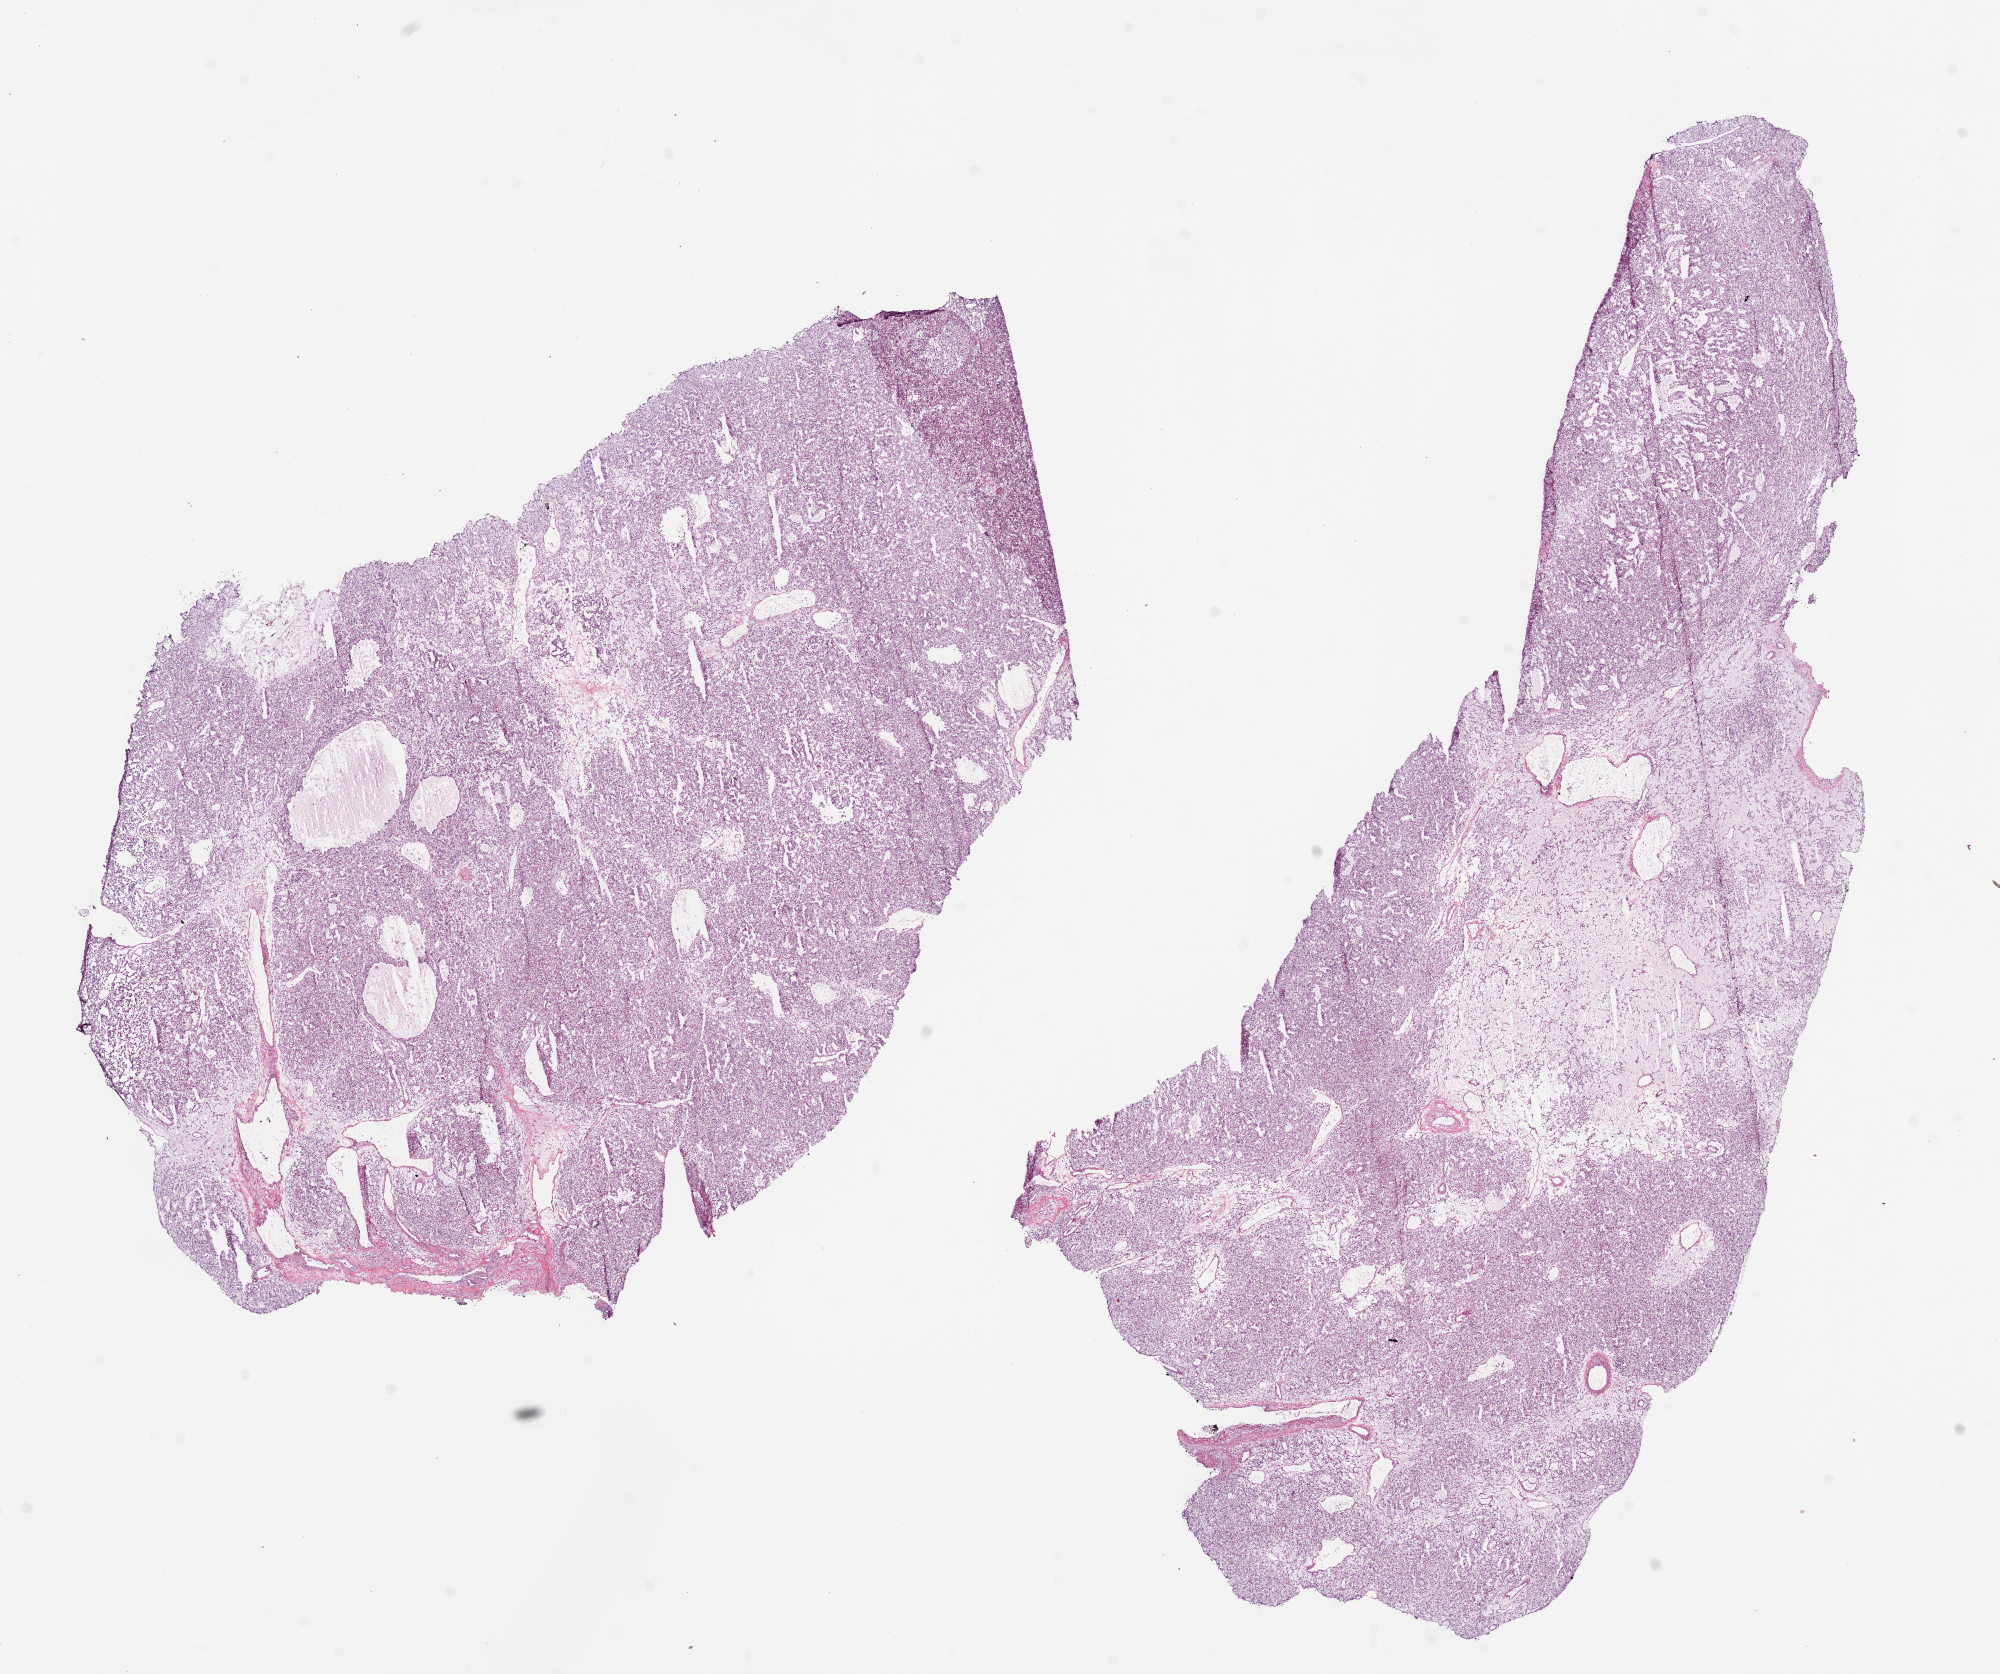
Digitized Hematoxylin and eosin (H&E) stained tissue section (whole slide), whole scanned area (about 16.0 x 13.4 mm, slide scanned at 20x) shown as a low-resolution overview. Frozen section. Primary tumour sample from the kidney. Male, age 77 years at initial diagnosis. Histologic grade: G3 (poorly differentiated). Slide review estimates, as recorded: tumour cells 75%, tumour nuclei 85%, normal cells 0%, stromal cells 25%, necrosis 0%.
• laterality: right
• histologic diagnosis: Clear cell adenocarcinoma, NOS
• AJCC pathologic stage: I